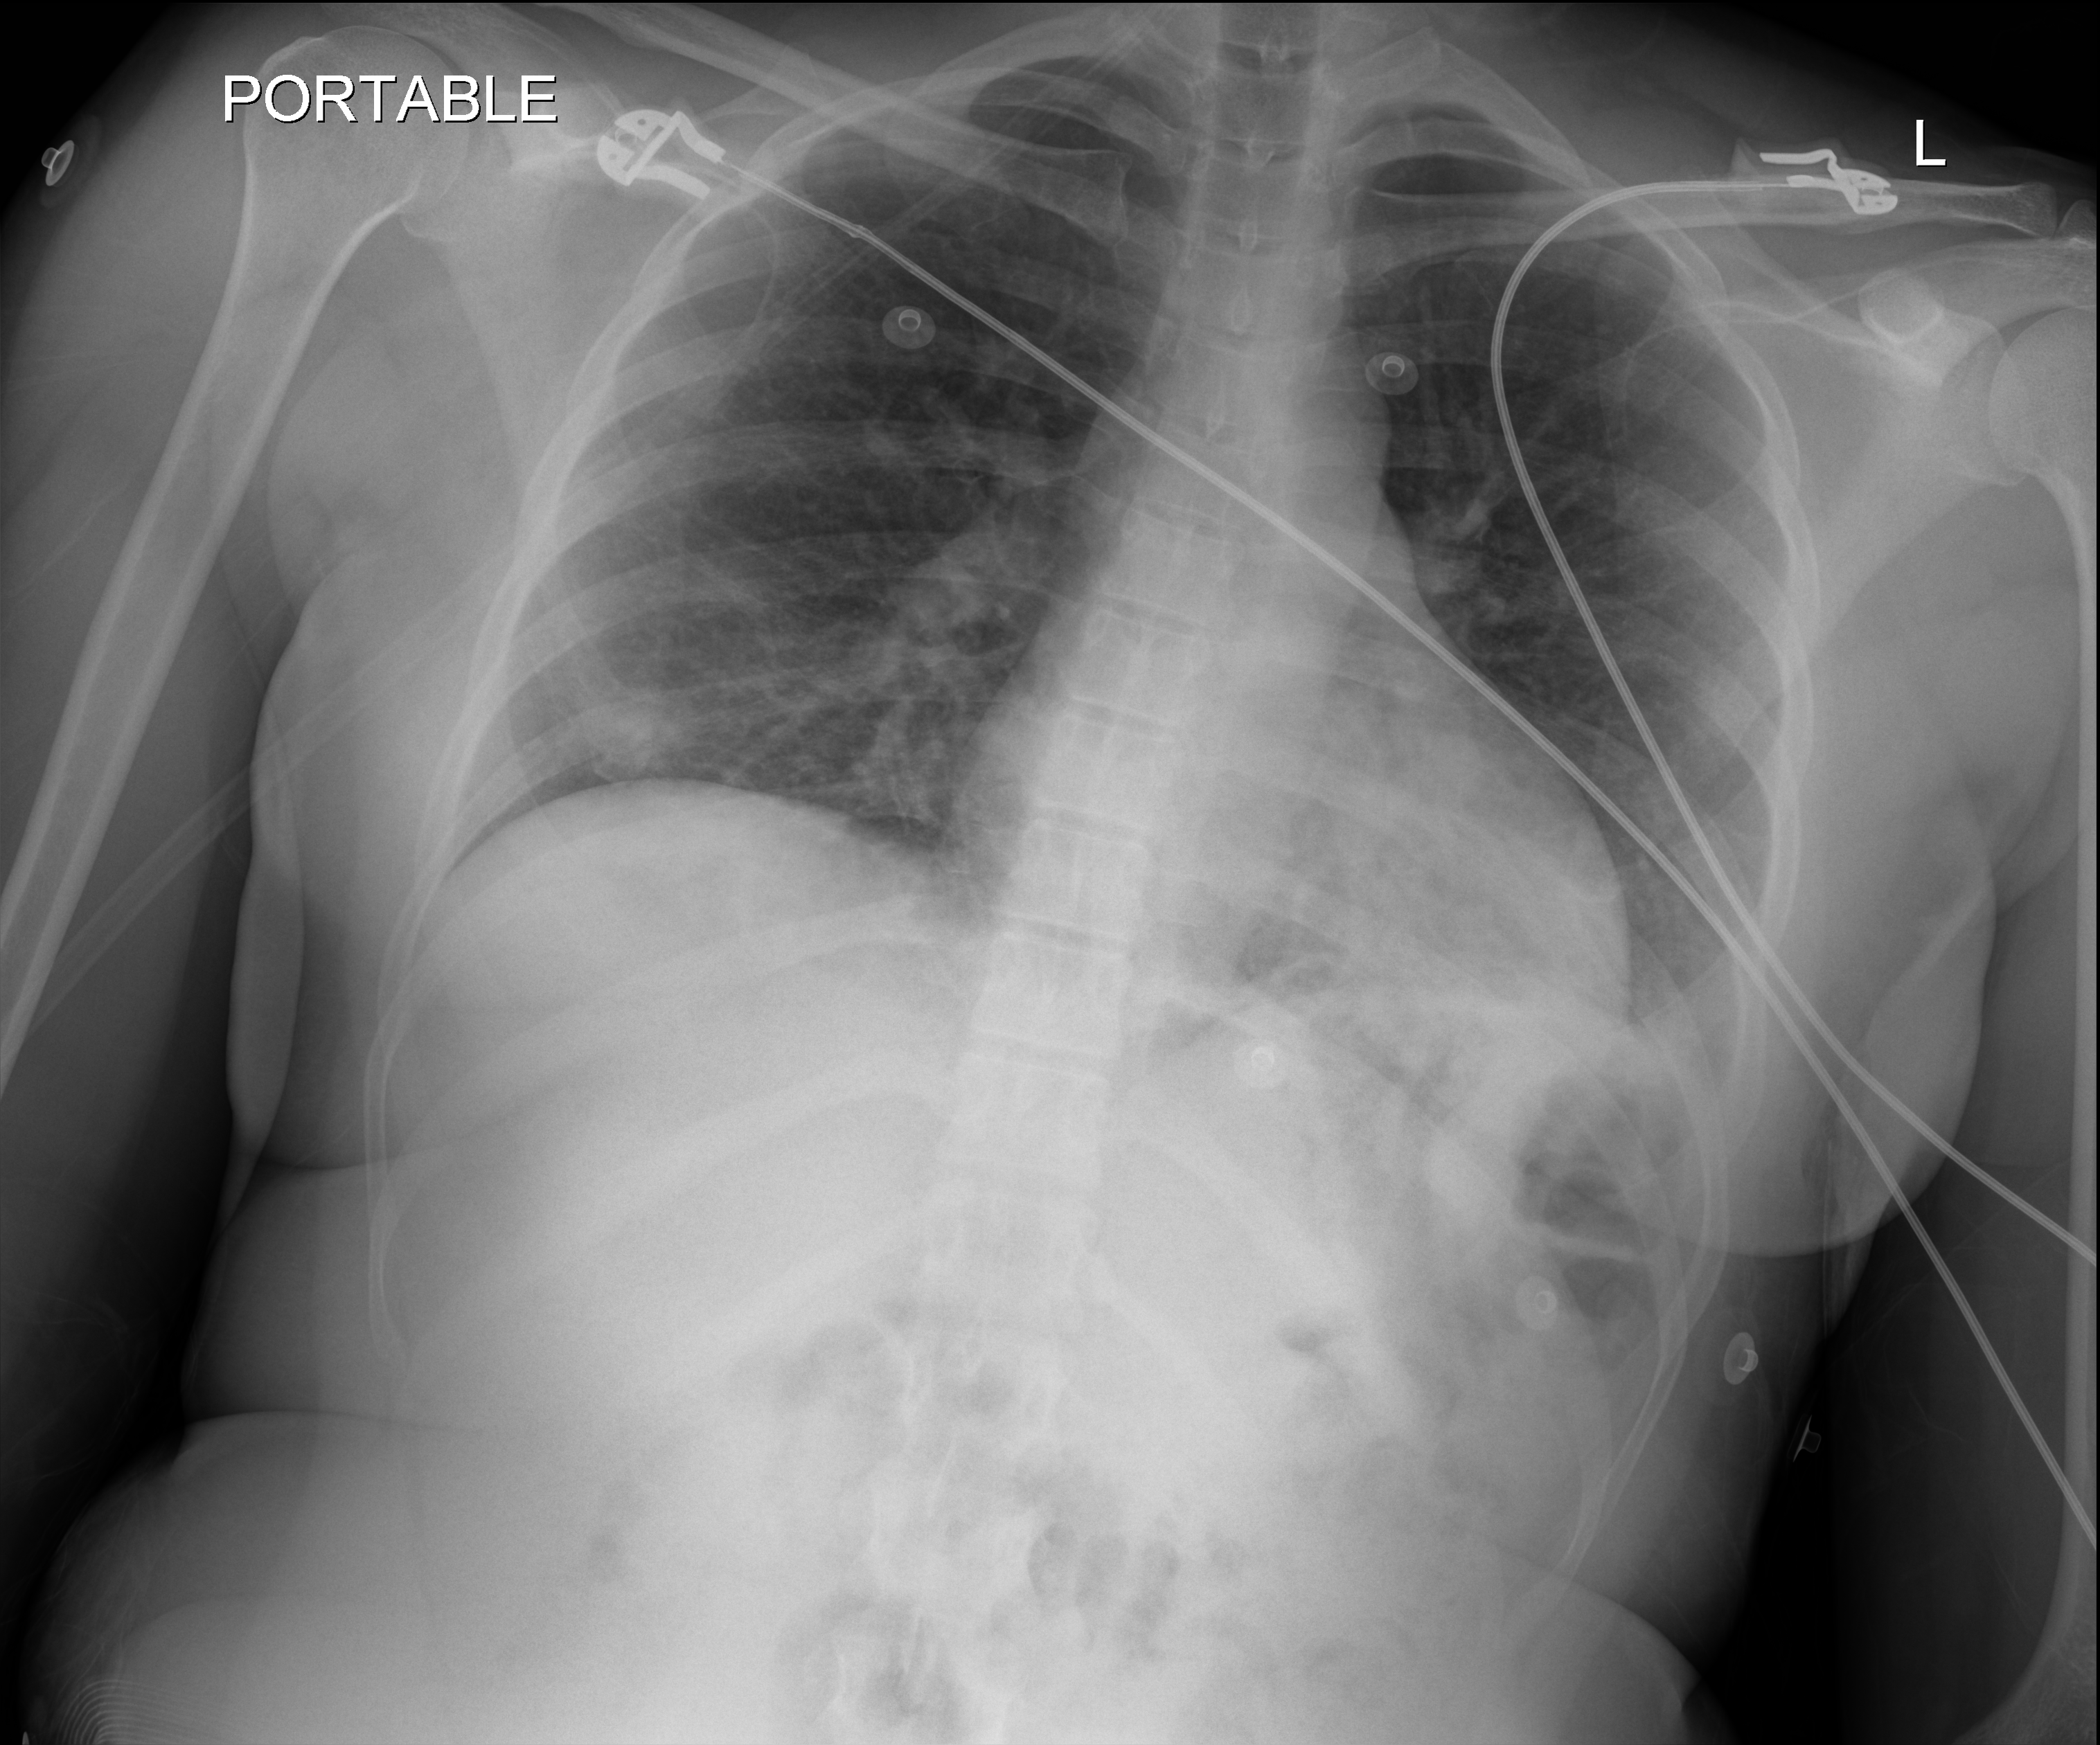
Chest radiograph (digital radiography), anteroposterior (AP) projection. Female patient hospitalised with COVID-19, age 18–59 years.
Admission-level facts for this patient (not findings on this image; timing relative to this image not recorded): mechanically ventilated during this hospital stay: no; admitted to intensive care during this hospital stay: no.